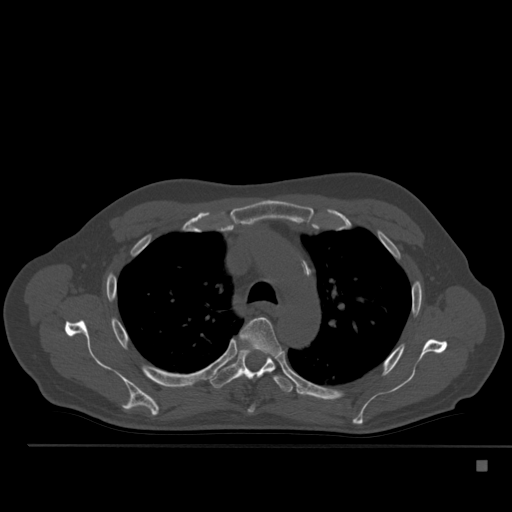
CT including the spine, one axial slice; slice 373 of 517 in the series (ordered by position); 120 kVp; bone window (W 1800 / L 400 HU); 1.5 mm slice thickness; 512 × 512 image matrix, field of view 408 × 408 mm. Male patient, age 70 years. From the clinical record (not read from this slice): primary cancer: renal; vertebrae with lytic lesions (as recorded): T4, T6, T10, T12, L3, L4, L5.
Structures marked on this image (semi-automatic segmentation, software-assisted and operator-edited):
- T4 vertebra: bounding box (x1, y1, x2, y2) in pixels: (240, 317, 281, 413)
- T5 vertebra: (210, 348, 295, 393)